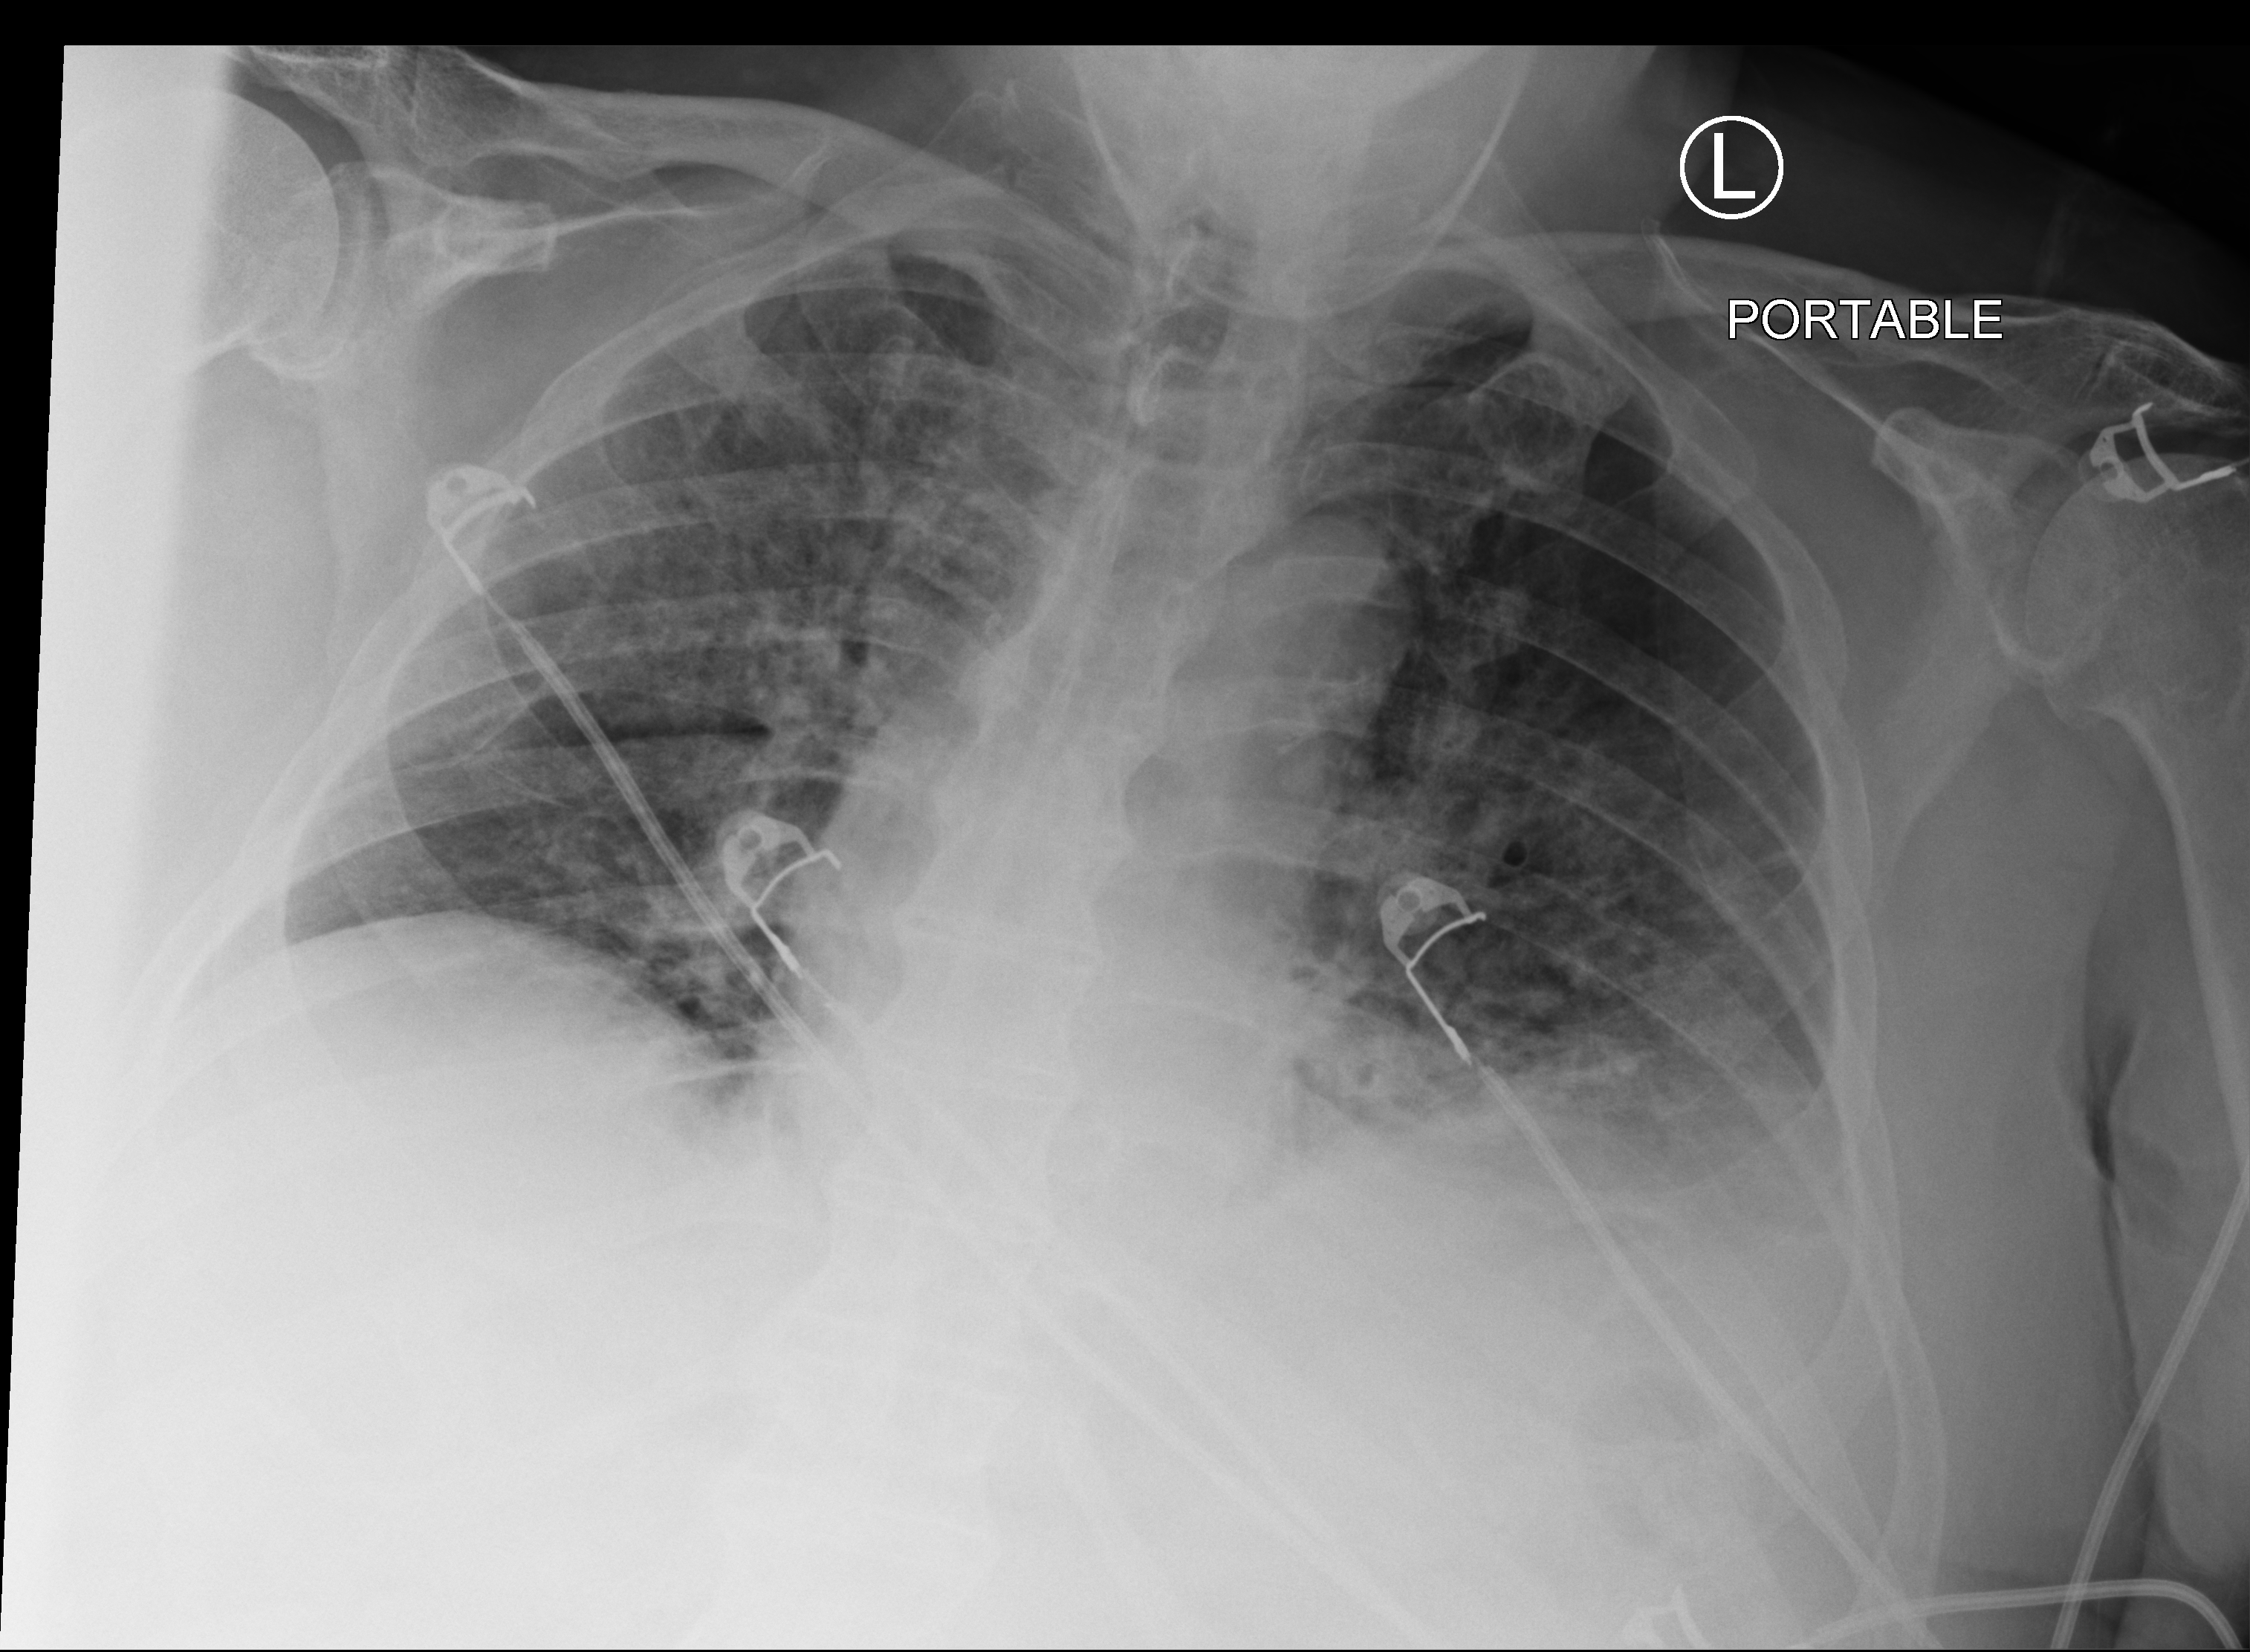
Portable chest radiograph. Male patient hospitalised with COVID-19, age 75–90 years.
Hospital-stay facts (about this admission, not read from this image; timing relative to this image not recorded): diabetes (admission record): no.